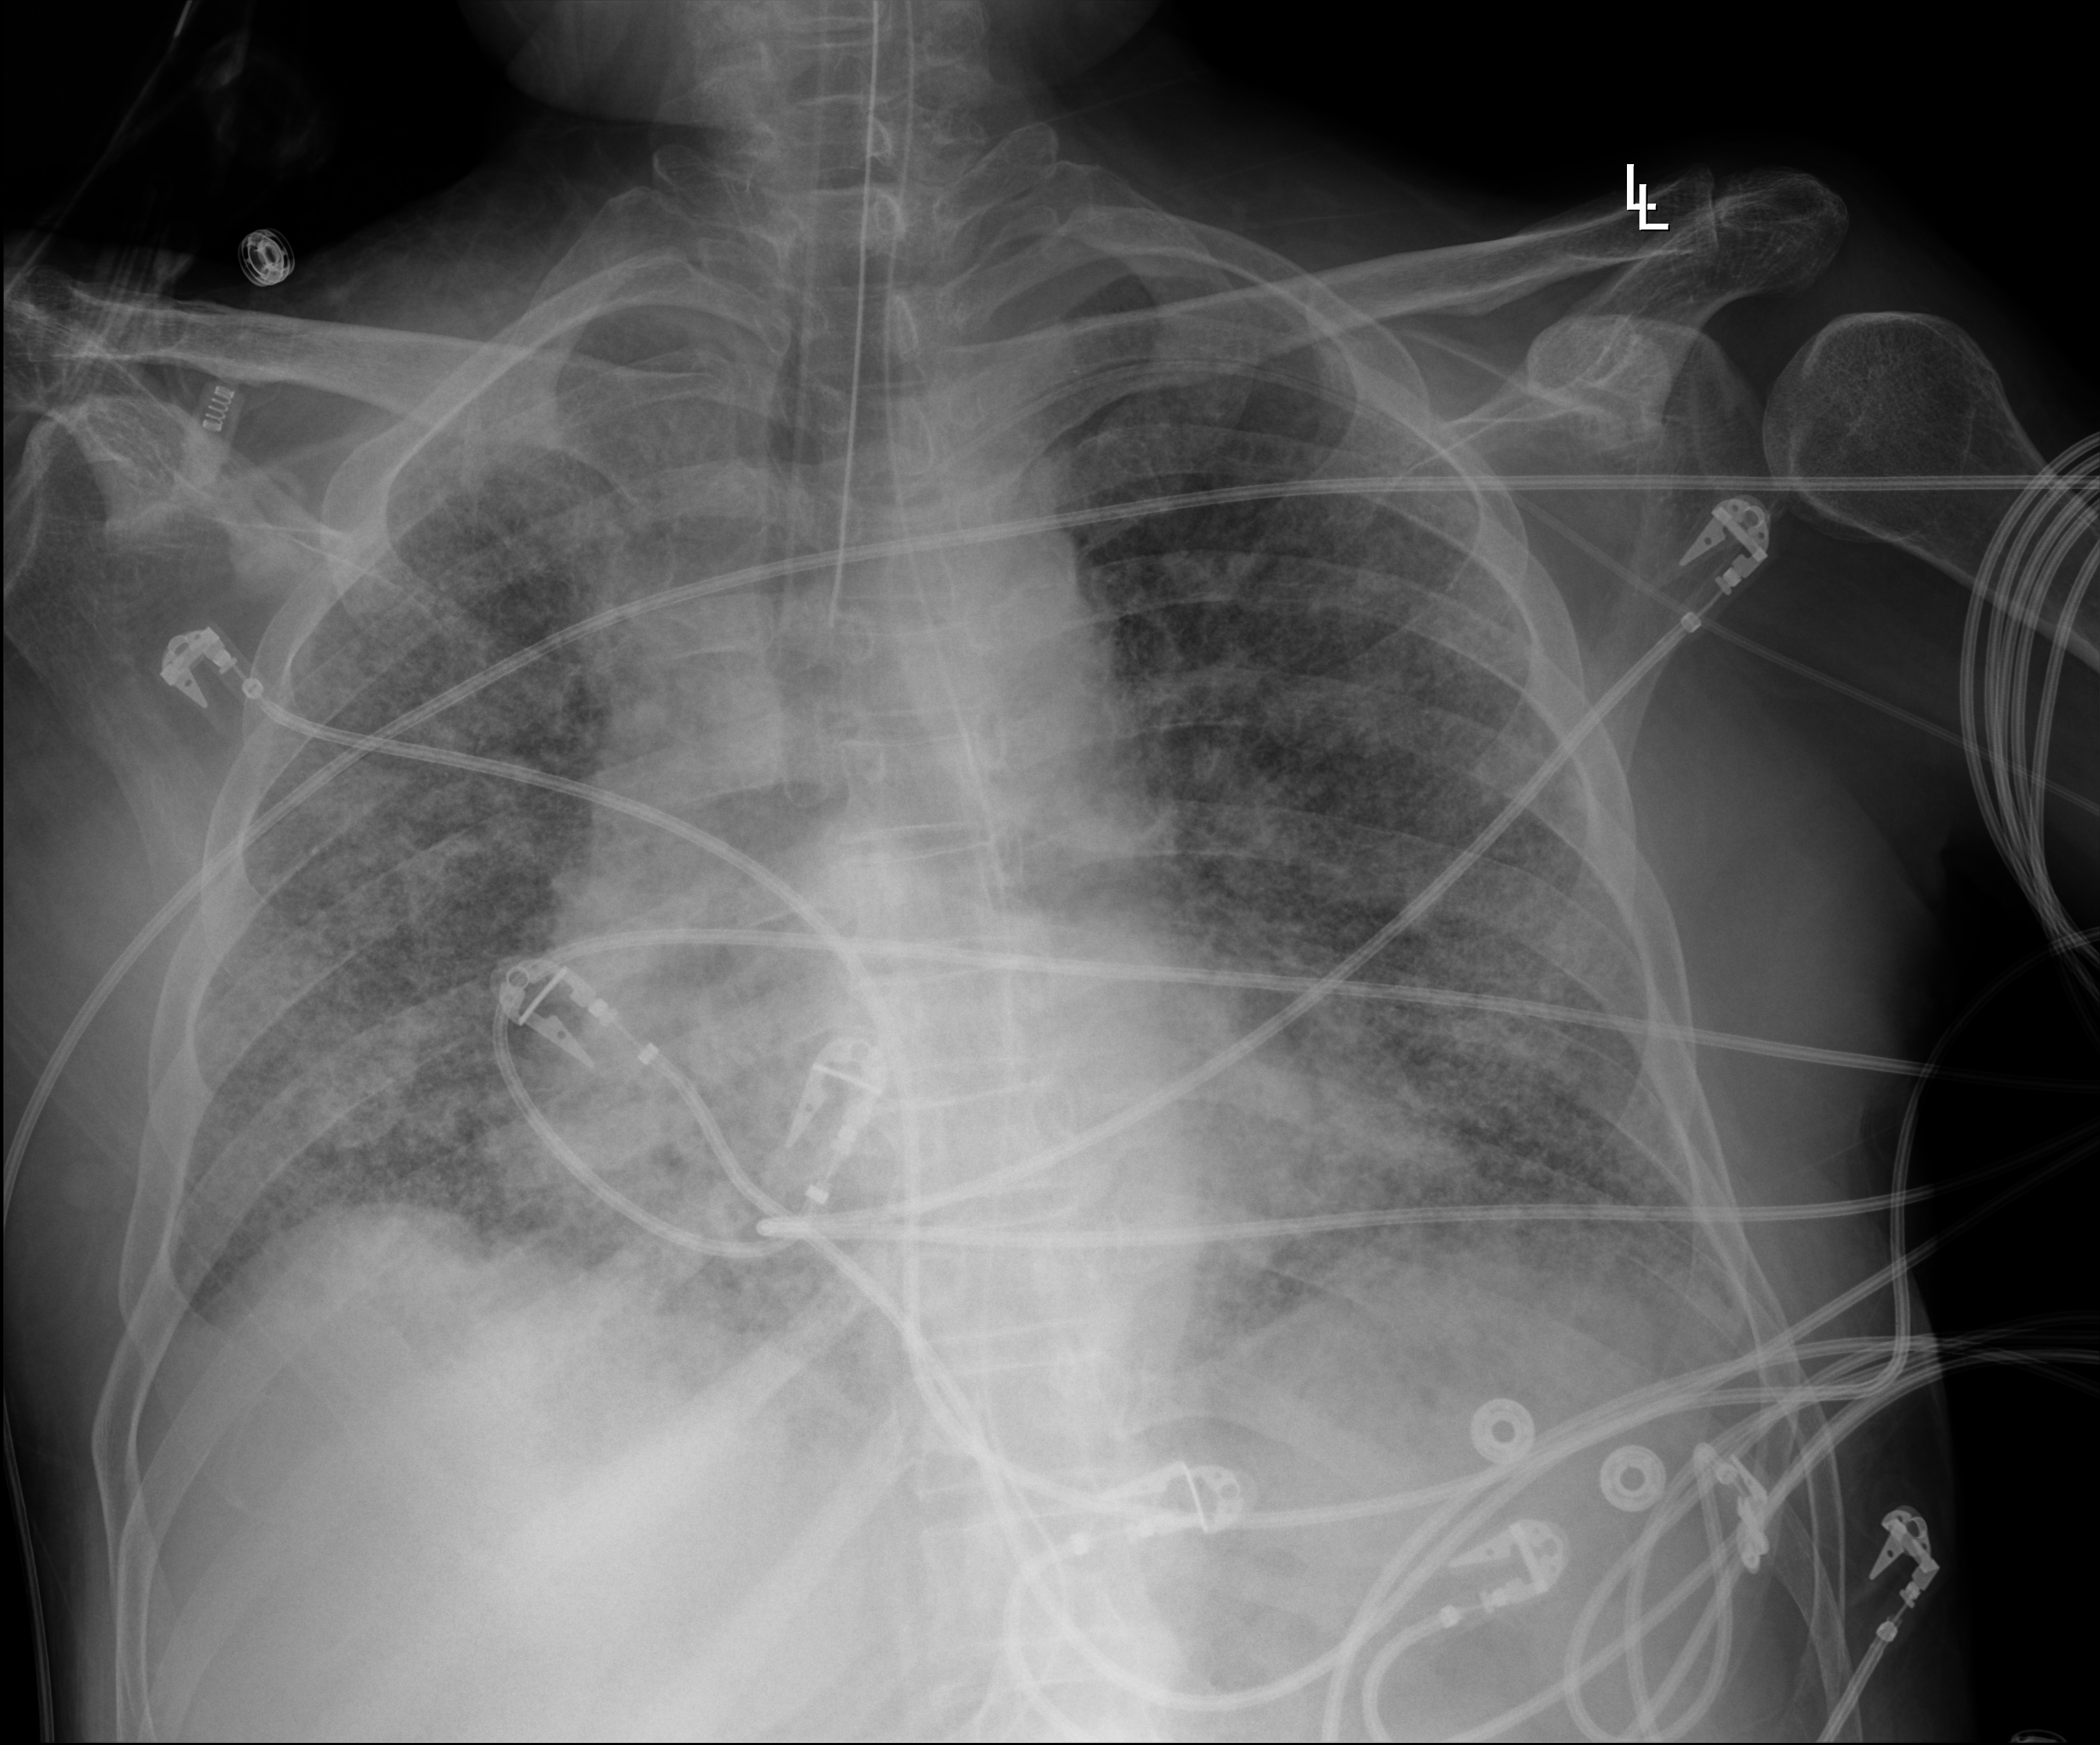
Chest radiograph. Male patient hospitalised with COVID-19, age 60–74 years.
Admission-level facts for this patient (not findings on this image; timing relative to this image not recorded):
- admitted to intensive care during this hospital stay: yes
- mechanically ventilated during this hospital stay: yes